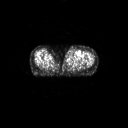
FDG PET of an extremity soft-tissue mass (from a PET/CT study), one axial slice. Slice 50 of 91 in the series (ordered by position). 3.27 mm slice thickness. 128 × 128 image matrix, field of view 700 × 700 mm. Patient: female, 74 years. Case-level facts recorded for this patient, not image findings: histological type: pleomorphic leiomyosarcoma; grade: high; site of the primary tumour: left thigh.
Outlined on this slice (expert contour drawn on MRI and transferred to this co-registered scan by the dataset authors):
- gross tumour volume including surrounding oedema: bounding box (x1, y1, x2, y2) in pixels: (65, 52, 77, 61)